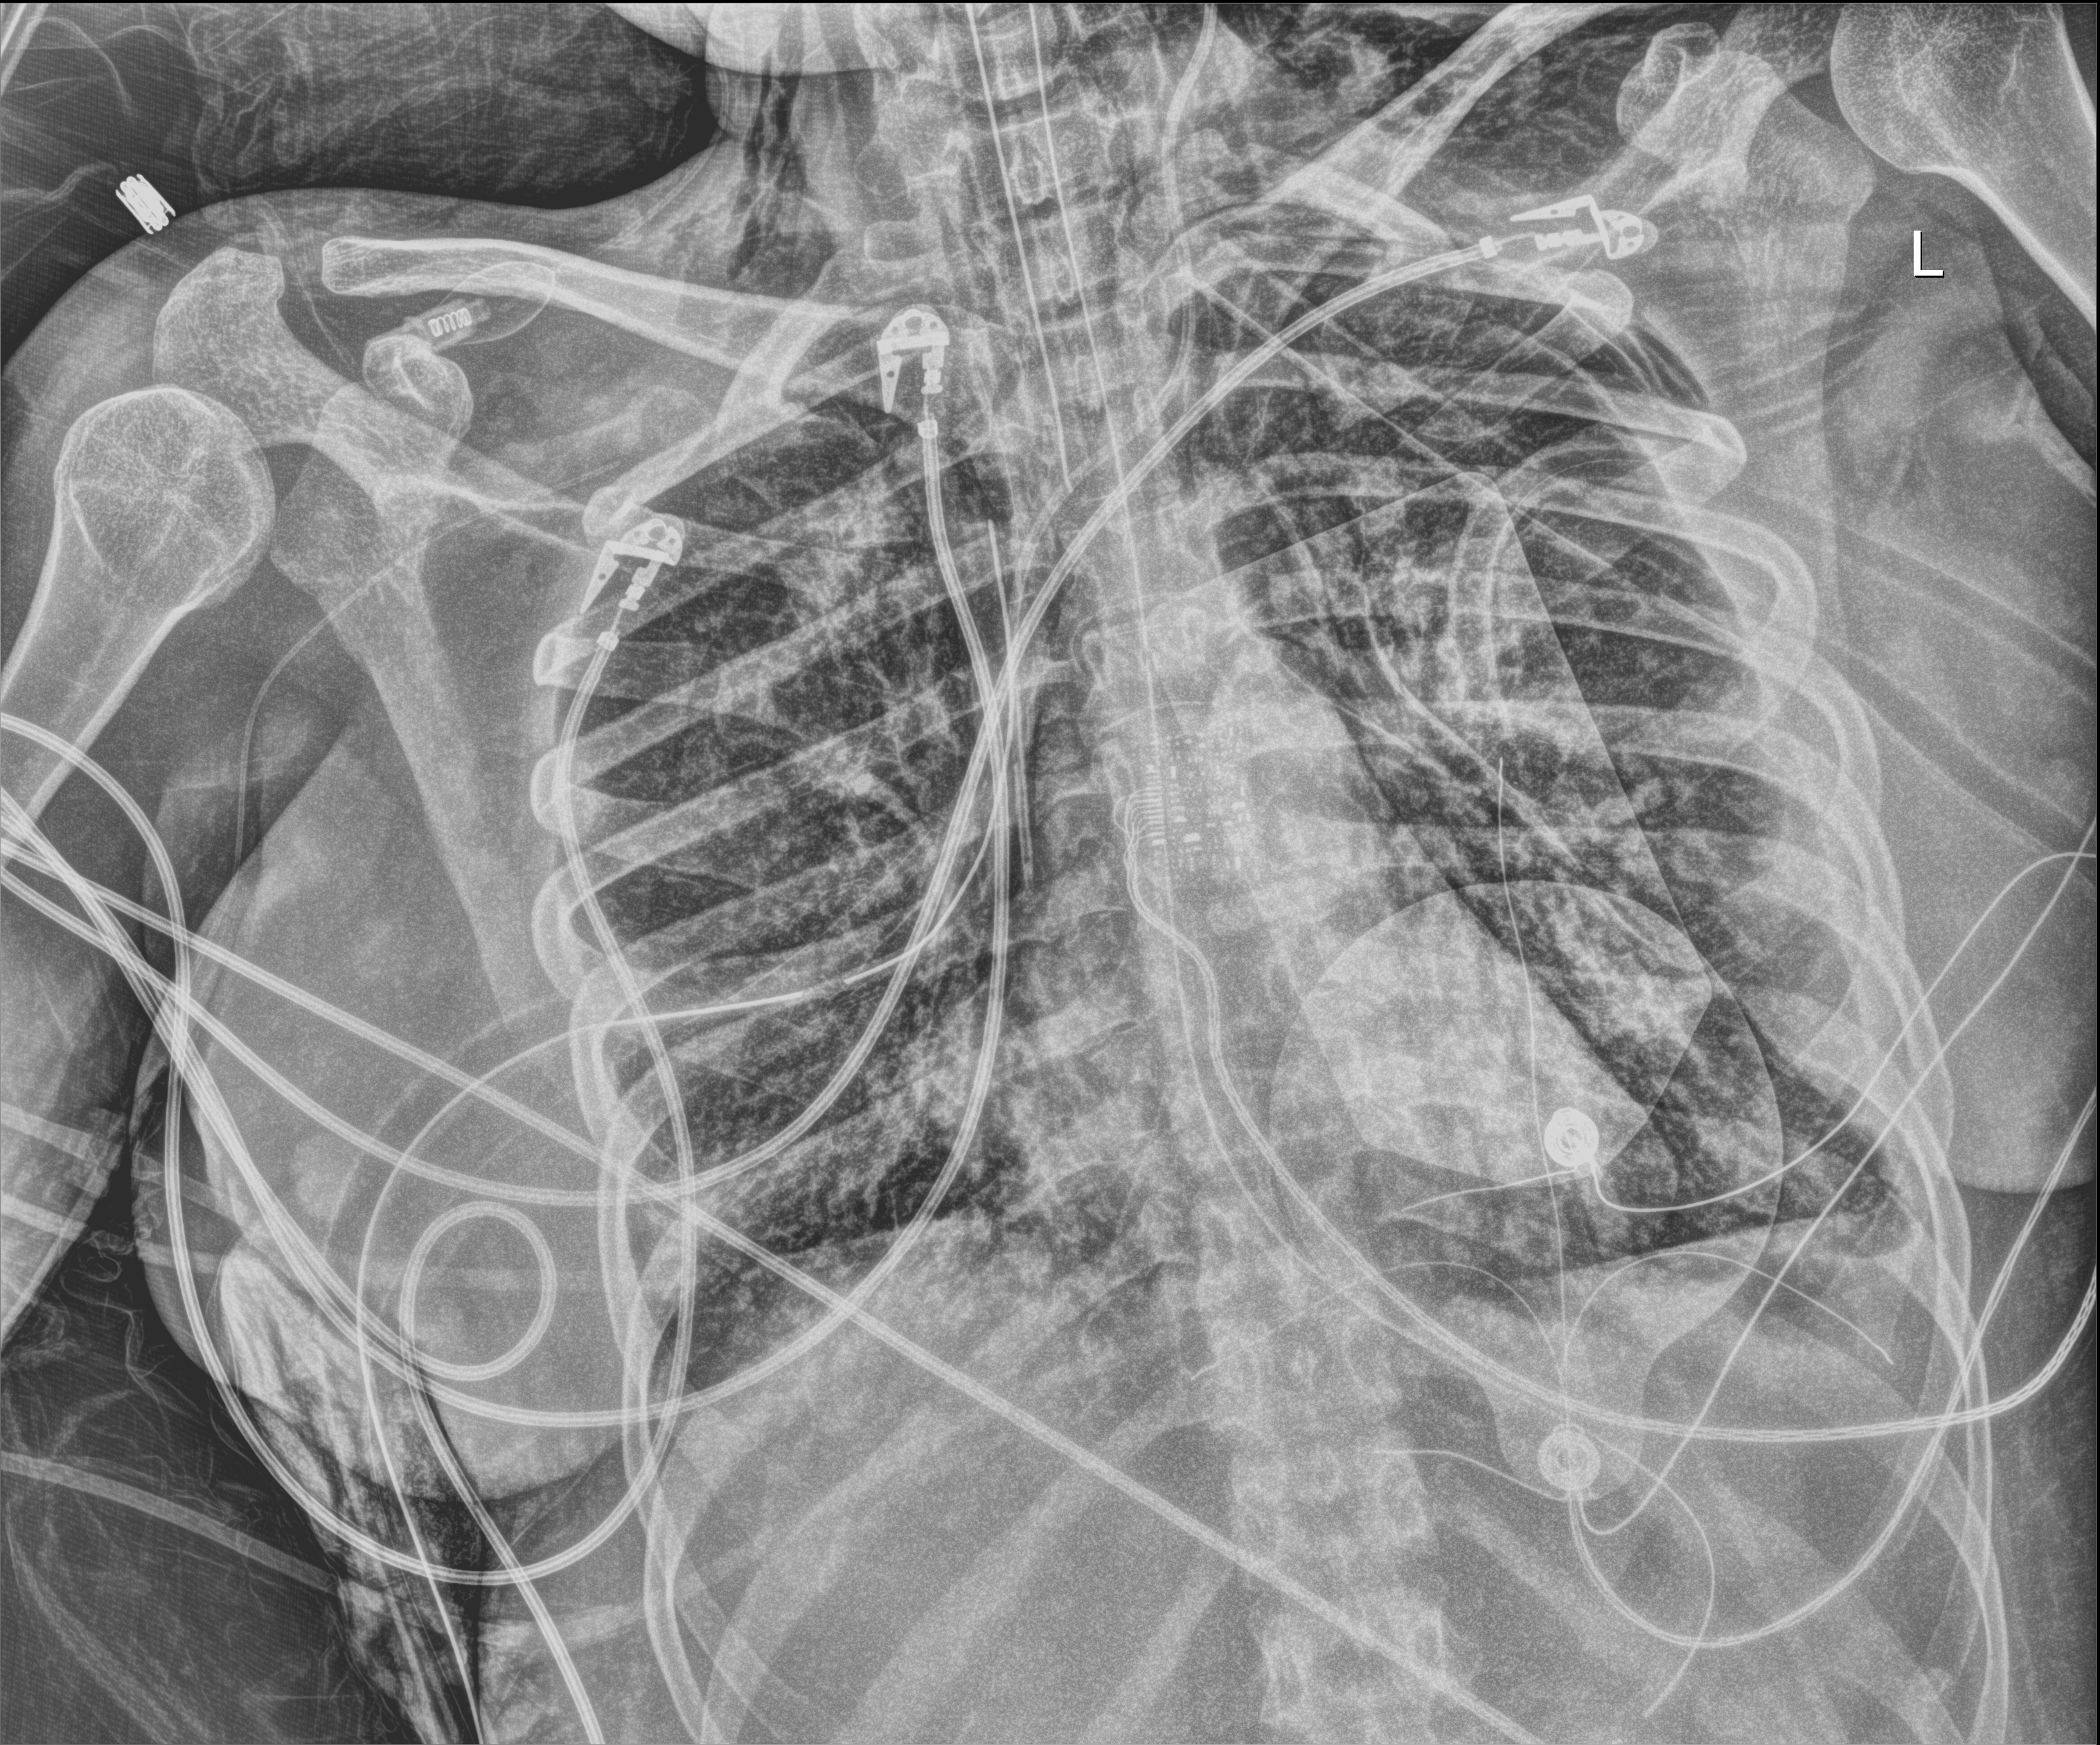
Chest radiograph (digital radiography). Patient hospitalised with COVID-19, aged 18–59 years.
Admission-level facts for this patient (not findings on this image; timing relative to this image not recorded):
- length of hospital stay: 30 days
- hypertension (admission record): no
- mechanically ventilated during this hospital stay: yes